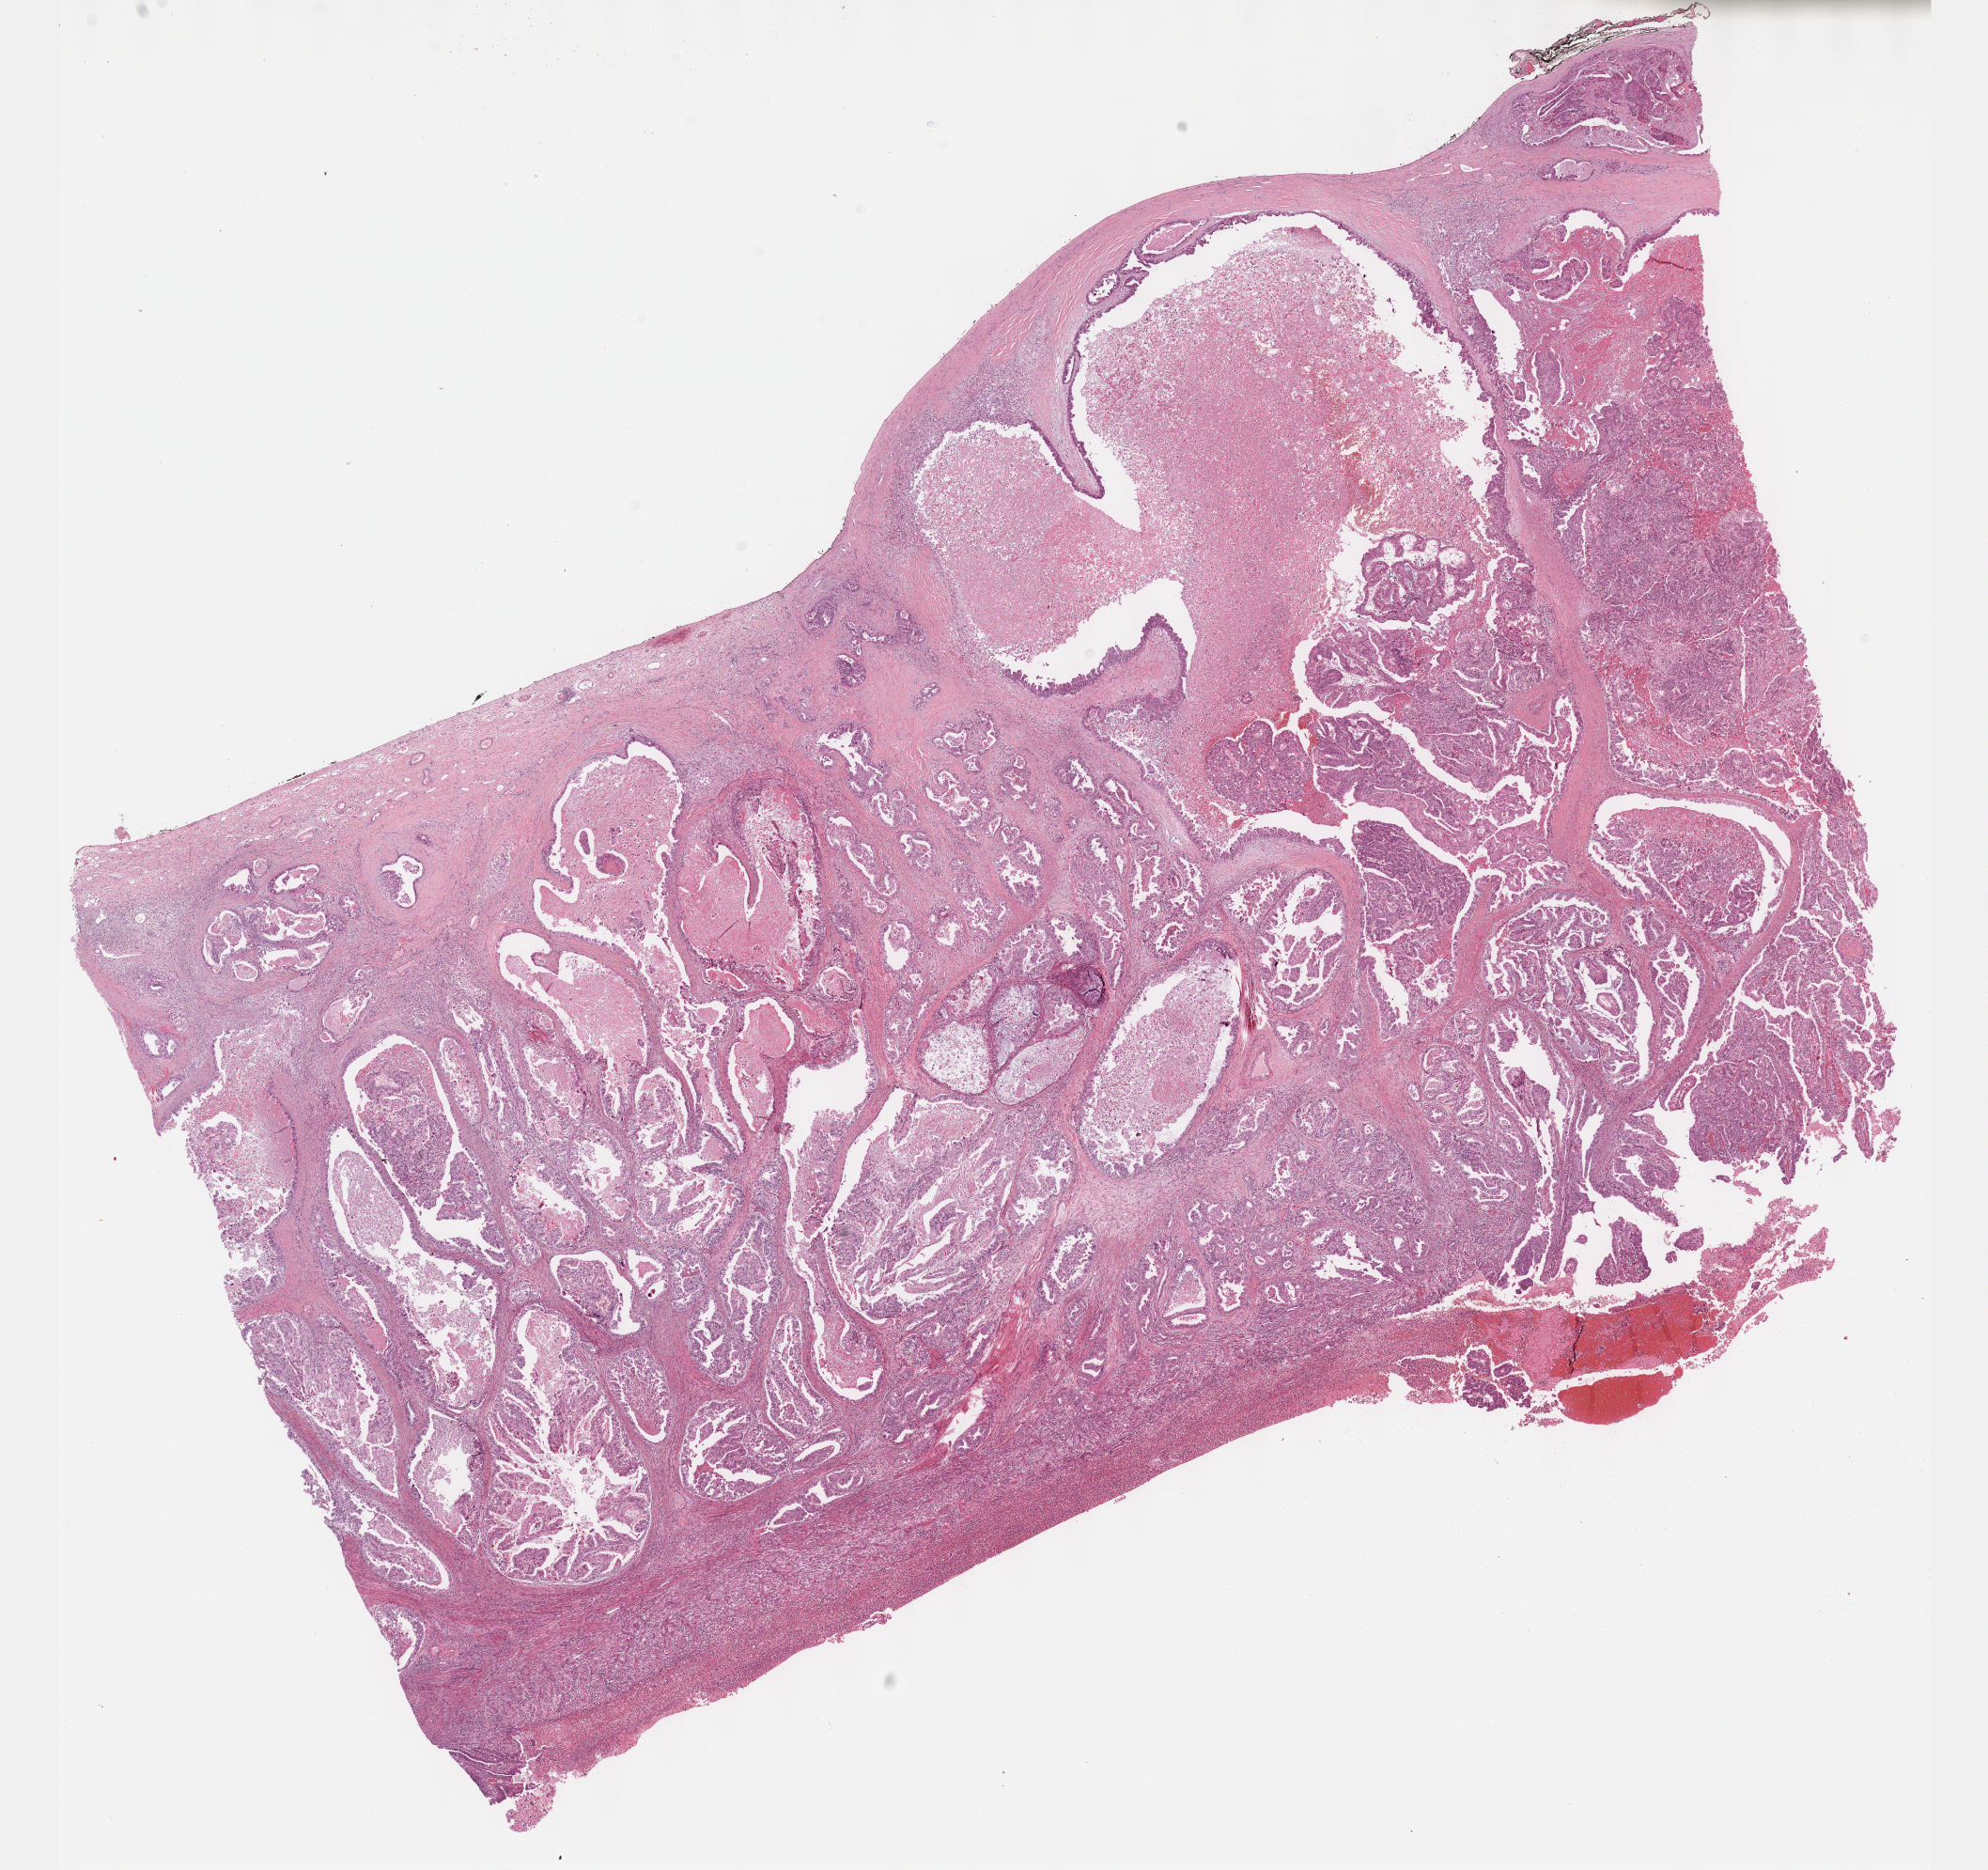
H&E whole-slide image, a low-resolution overview of the entire scanned area, about 17.1 x 16.1 mm (from a 40x scan). Formalin-fixed paraffin-embedded (FFPE) diagnostic section. Primary tumour sample from the stomach. Patient: male, age at initial diagnosis 53 years. Histologic grade: GX (grade cannot be assessed).
Histologic diagnosis: Tubular adenocarcinoma (body of stomach). AJCC pathologic stage: IV (6th edition). Lymph nodes positive (case pathology): 9 of 24 examined.